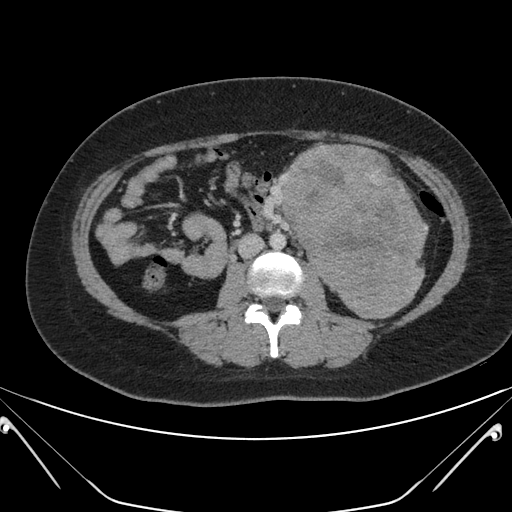
Contrast-enhanced abdominal CT, one axial slice; slice 95 of 168 in the series (ordered by position); intravenous contrast given; soft-tissue window (W 400 / L 40 HU); 3 mm slice thickness; 512 × 512 image matrix, field of view 394 × 394 mm. Female patient, age 26 years. Case-level facts recorded for this patient, not image findings: diagnosis: adrenocortical carcinoma; tumour side: left adrenal; tumour size at pathology: 28 cm; Ki-67 index: 20 %; stage (as recorded): 2.
Annotated regions visible in this slice (semi-automatically segmented with operator editing):
- mass: box from (x=286, y=146) to (x=423, y=316) px